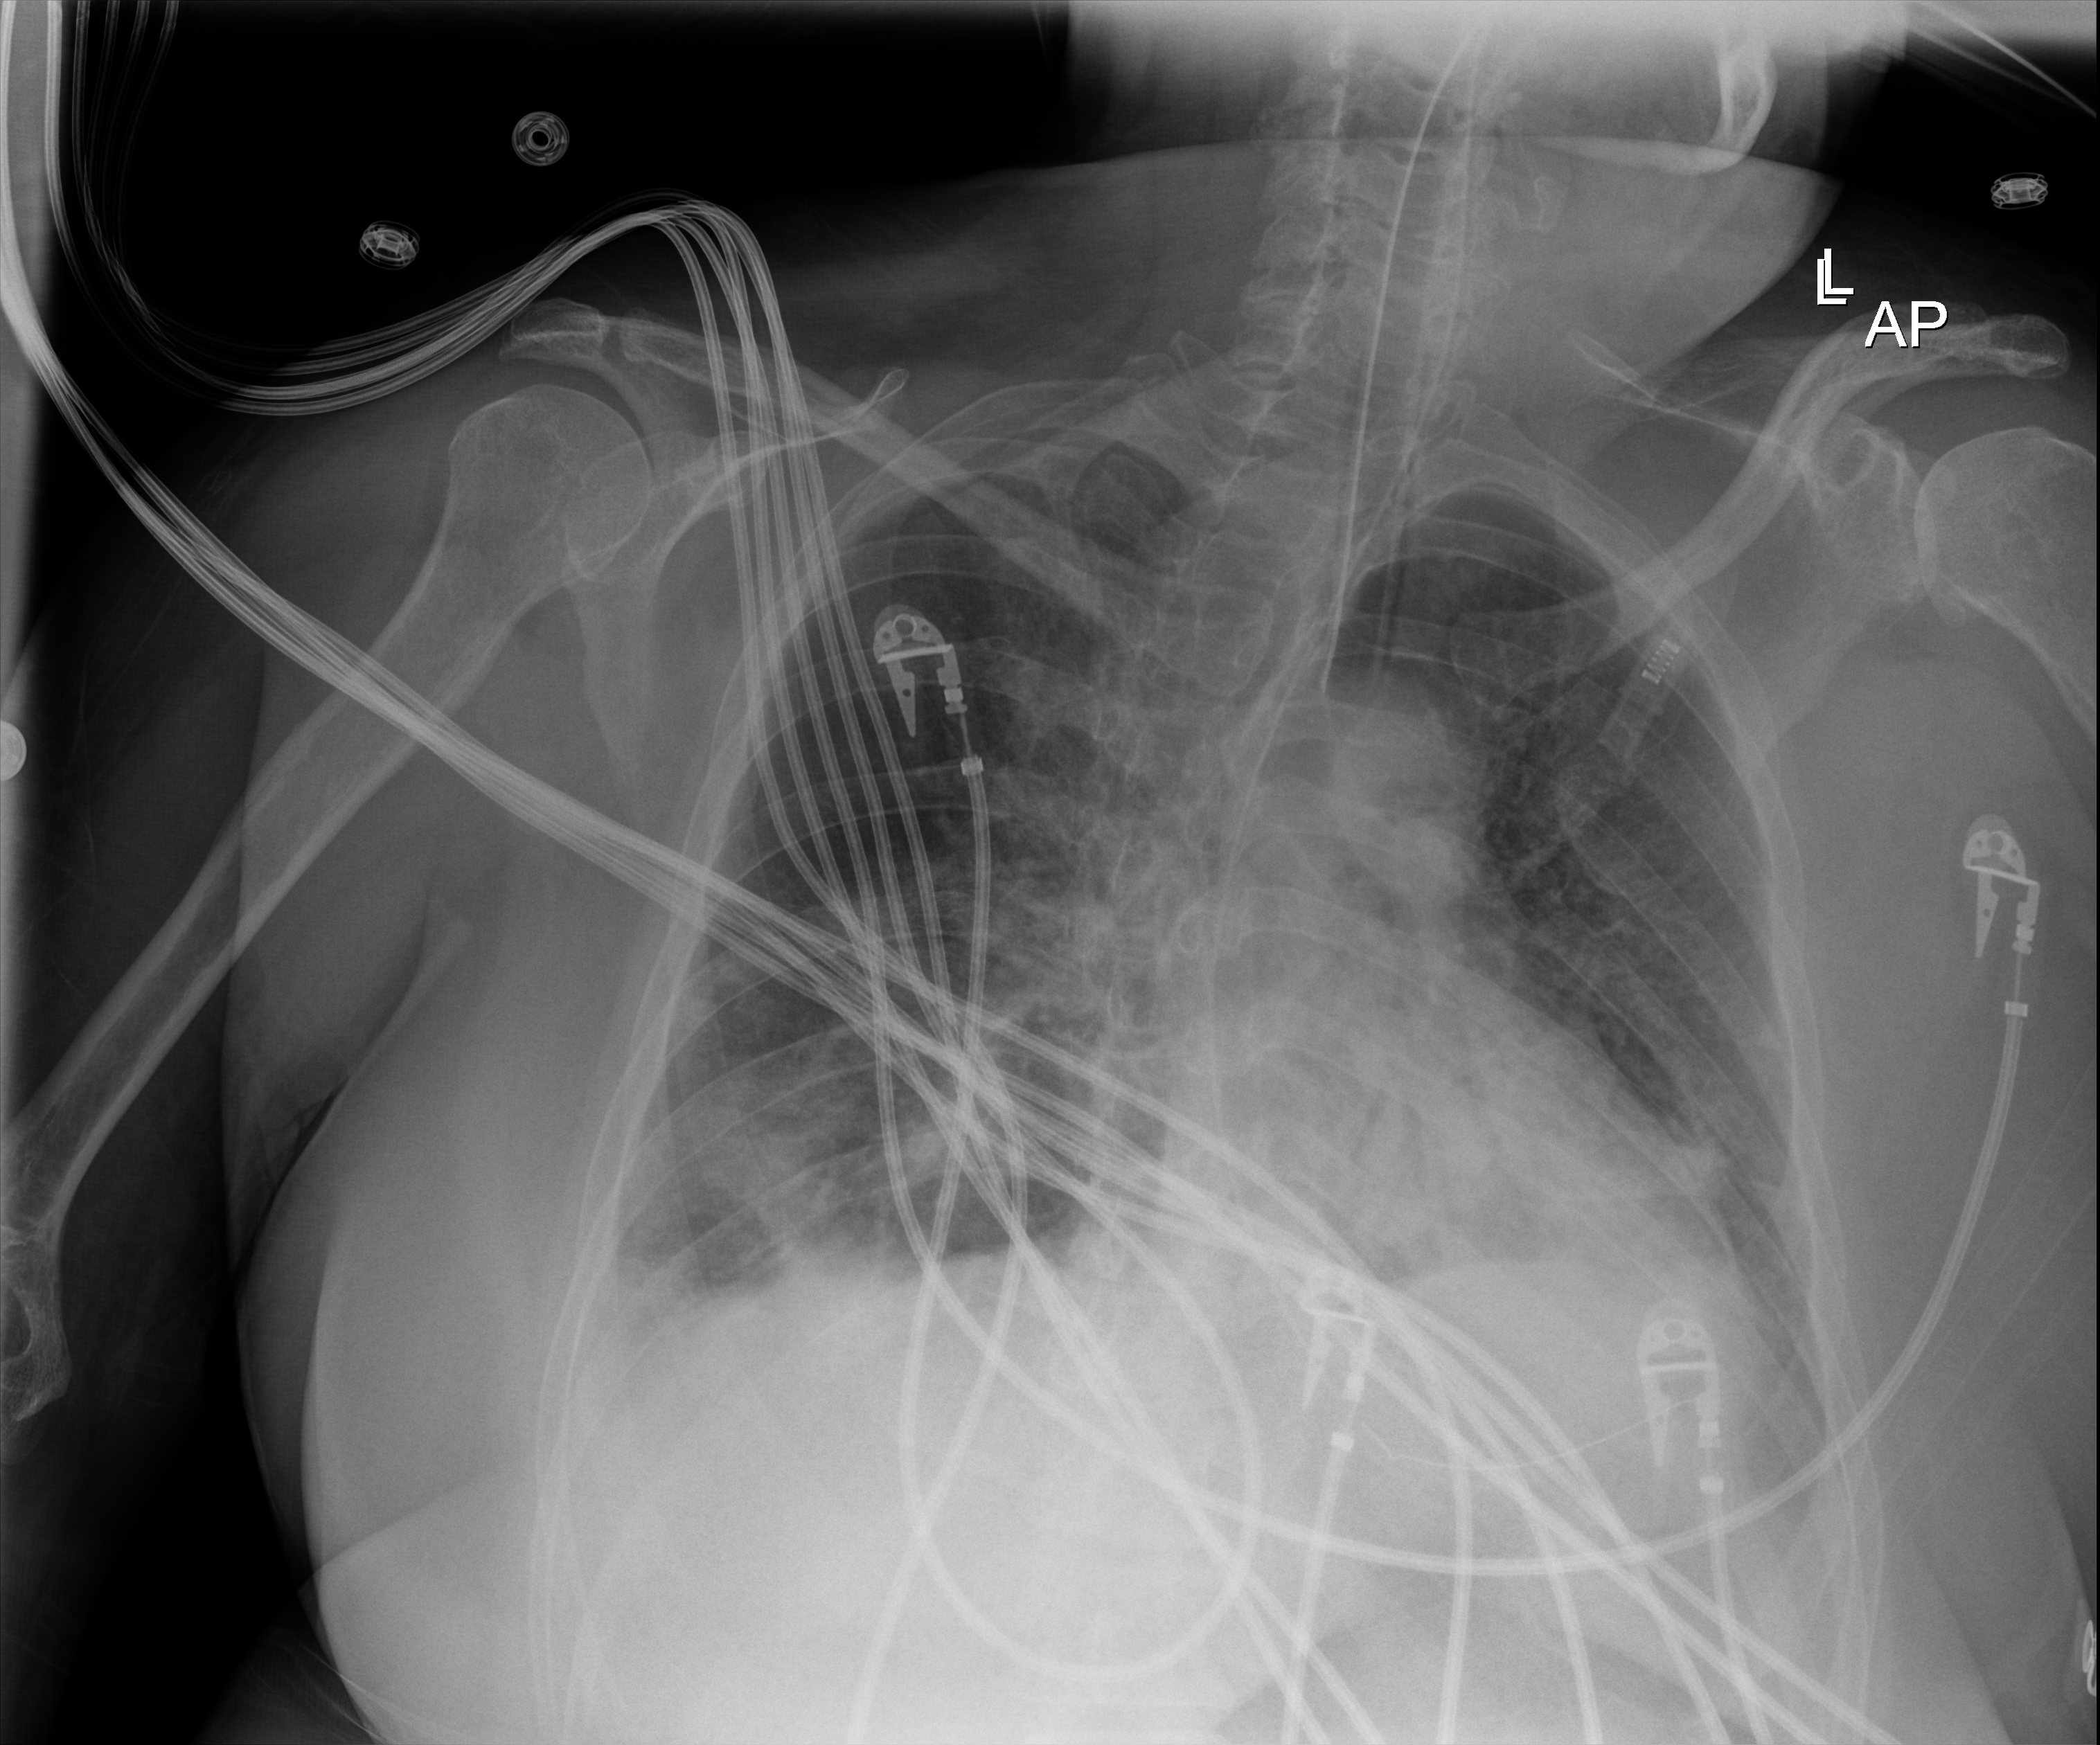
Portable chest radiograph, anteroposterior (AP) projection. Adult patient hospitalised with COVID-19, age 18–59 years.
Admission-level facts for this patient (not findings on this image; timing relative to this image not recorded): mechanically ventilated during this hospital stay: yes; admitted to intensive care during this hospital stay: yes.